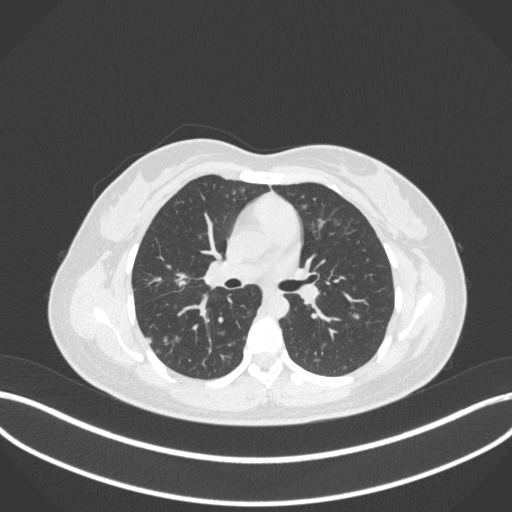
Chest CT, one axial slice. Position 194 of 214 along the scan axis. Reconstruction kernel B31f. Lung window (W 1500 / L -600 HU). 1 mm slice thickness. 512 × 512 image matrix. Patient: female, 33 years. From the clinical record (not read from this slice): clinical TNM (as recorded): T1c N0 M0; histopathological grade: G2-G3.
Outlined on this slice (bounding box drawn by a radiologist):
- lung tumour (recorded histology: adenocarcinoma): box from (x=170, y=269) to (x=189, y=291) px